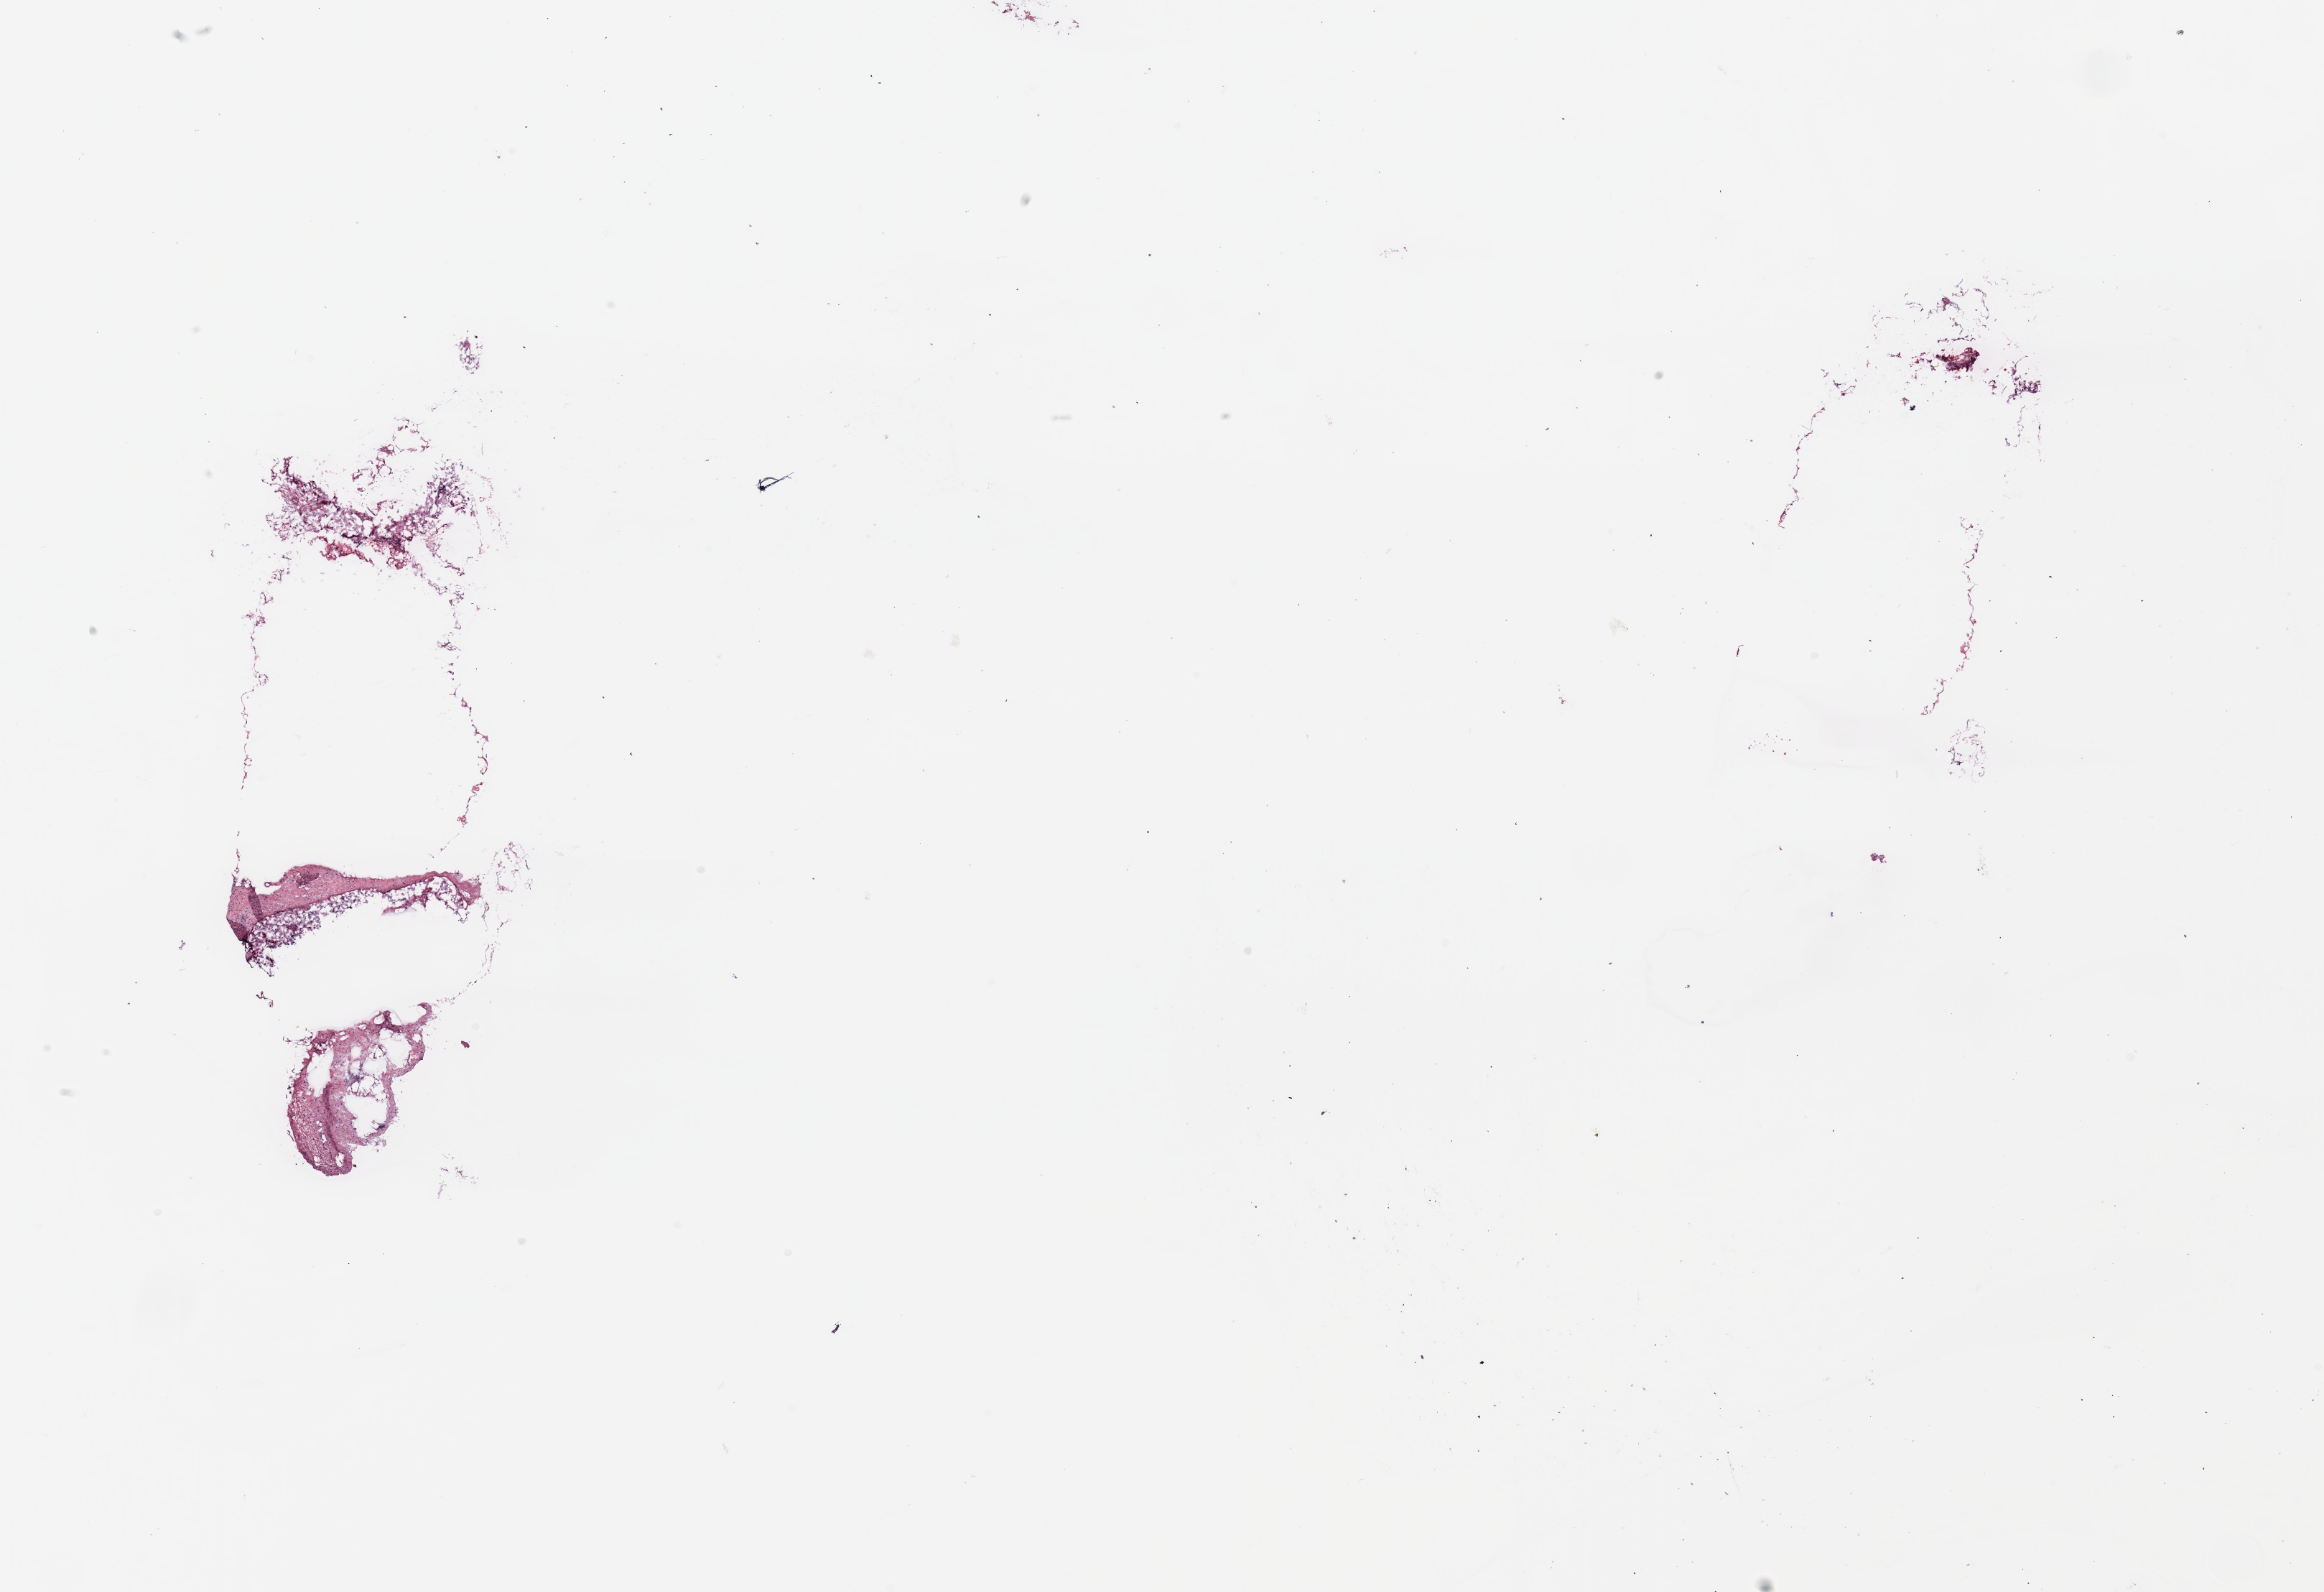
Hematoxylin and eosin (H&E) stained whole-slide image — whole scanned area (about 25.6 x 17.5 mm, slide scanned at 20x) shown as a low-resolution overview; breast, tissue type not recorded.
Patient diagnosis (cohort enrolment): breast cancer (breast).